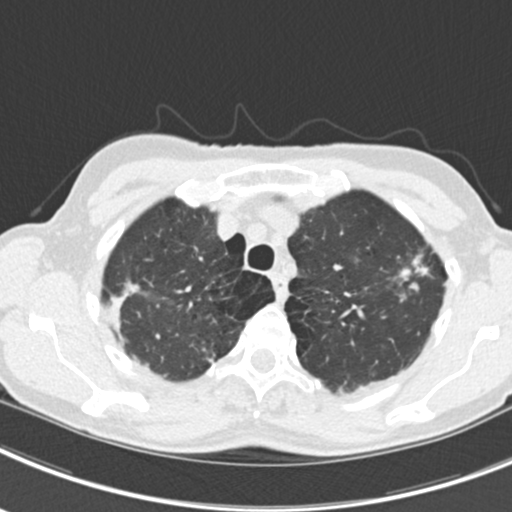
Chest CT (low-dose screening protocol), one axial image, second screening round (one year after baseline), lung window (W 1500 / L -600 HU), standard (soft-tissue) reconstruction kernel (B30f), 512 × 512 image matrix, field of view 298 × 298 mm. Female participant, aged 63 years at enrolment. Current smoker at enrolment.
Lesion marked by an expert reader, bounding box <383,240,449,302> (left, top, right, bottom; pixels). The screening reader recorded 9 non-calcified nodules or masses ≥4 mm on this exam (left upper lobe, right upper lobe, left upper lobe, left lower lobe, right middle lobe, left lower lobe, left lower lobe, right lower lobe, right lower lobe); which of them this box marks is not recorded. Official screen result: positive, other. Participant outcome: lung cancer diagnosed 408 days after this screen — bronchiolo-alveolar adenocarcinoma, NOS, right upper lobe, right middle lobe, right lower lobe, left upper lobe, left lower lobe, moderately differentiated (G2), stage IV (AJCC 6th edition).